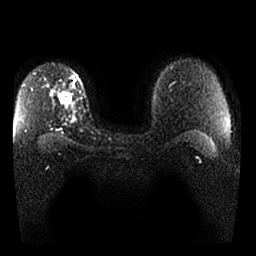
Breast MRI, one axial slice; position 20 of 25 along the scan axis; diffusion-weighted series; image 2 of 4 stored at this slice position (different b-values; order by instance number); 1.5 T; 4 mm slice thickness; 256 × 256 image matrix, field of view 340 × 340 mm. Female patient.
Outlined on this slice (manually delineated by an expert):
- tumour on diffusion-weighted imaging: bounding box <58,94,73,105> (left, top, right, bottom; pixels)